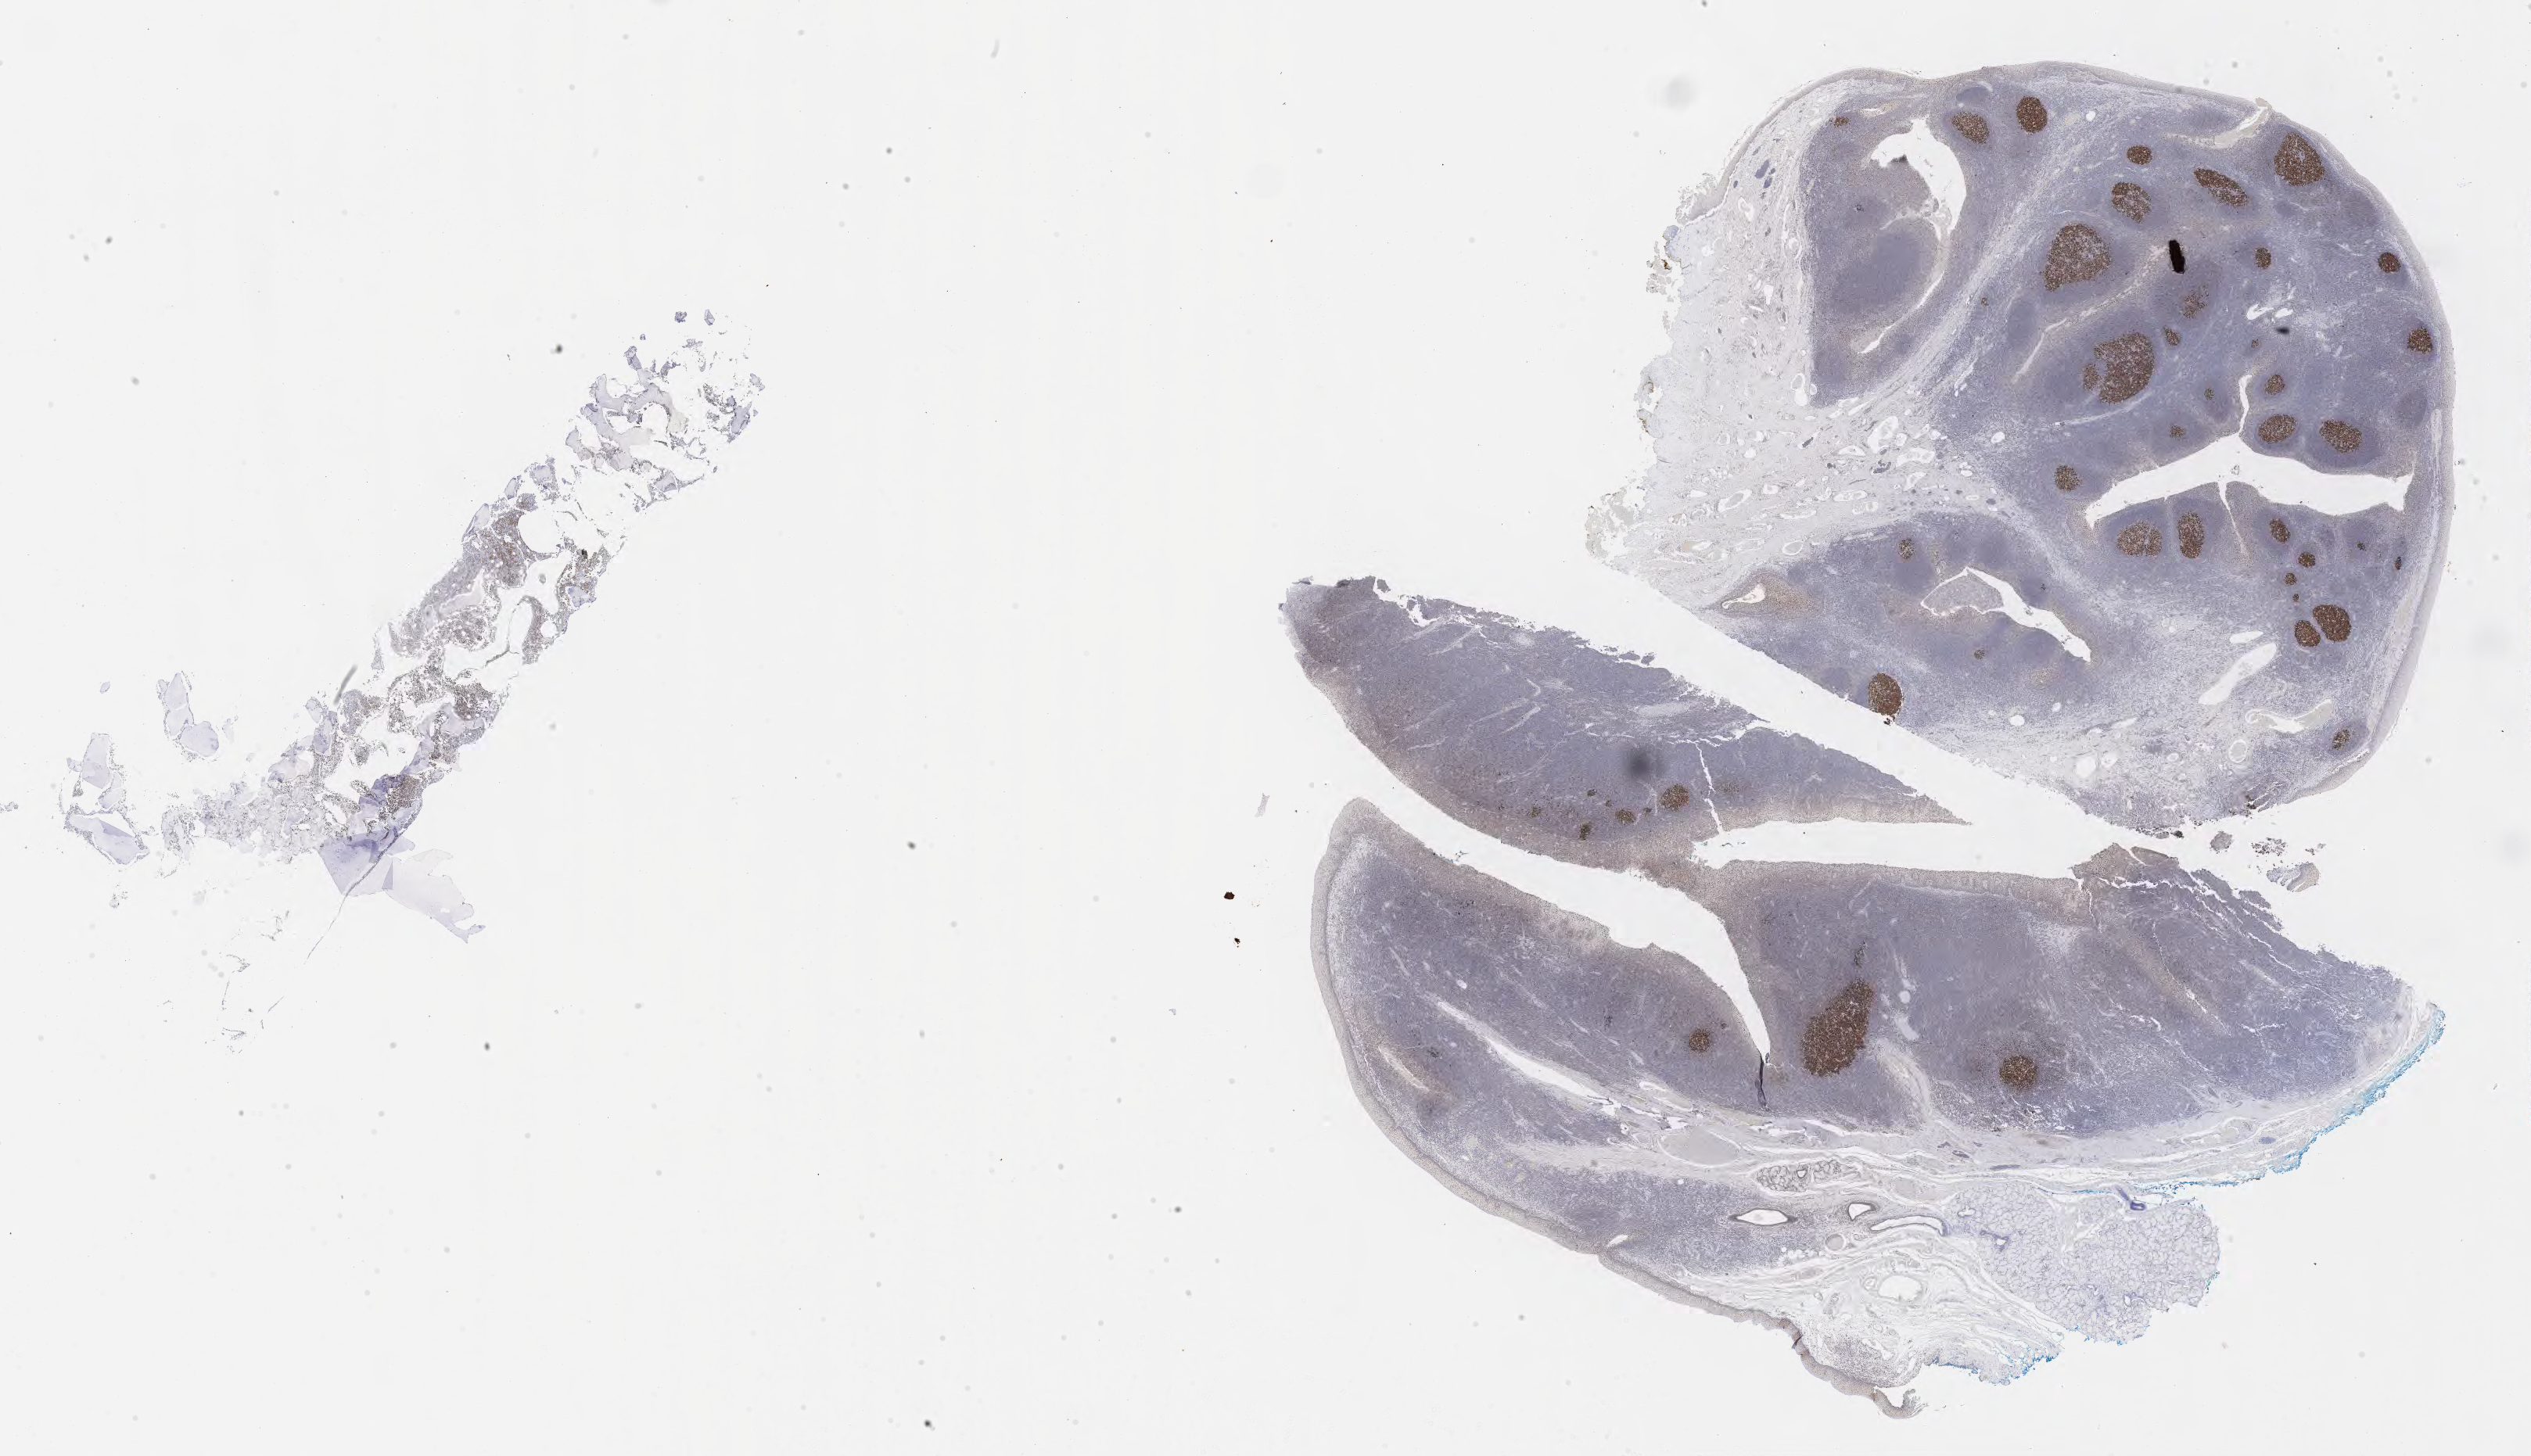
Immunohistochemistry (IHC) whole-slide image stained for BCL6, a low-resolution overview of the entire scanned area, about 26.2 x 15.1 mm; tumor tissue. Patient male; 13 years old.
Histologic diagnosis: Burkitt lymphoma, NOS.